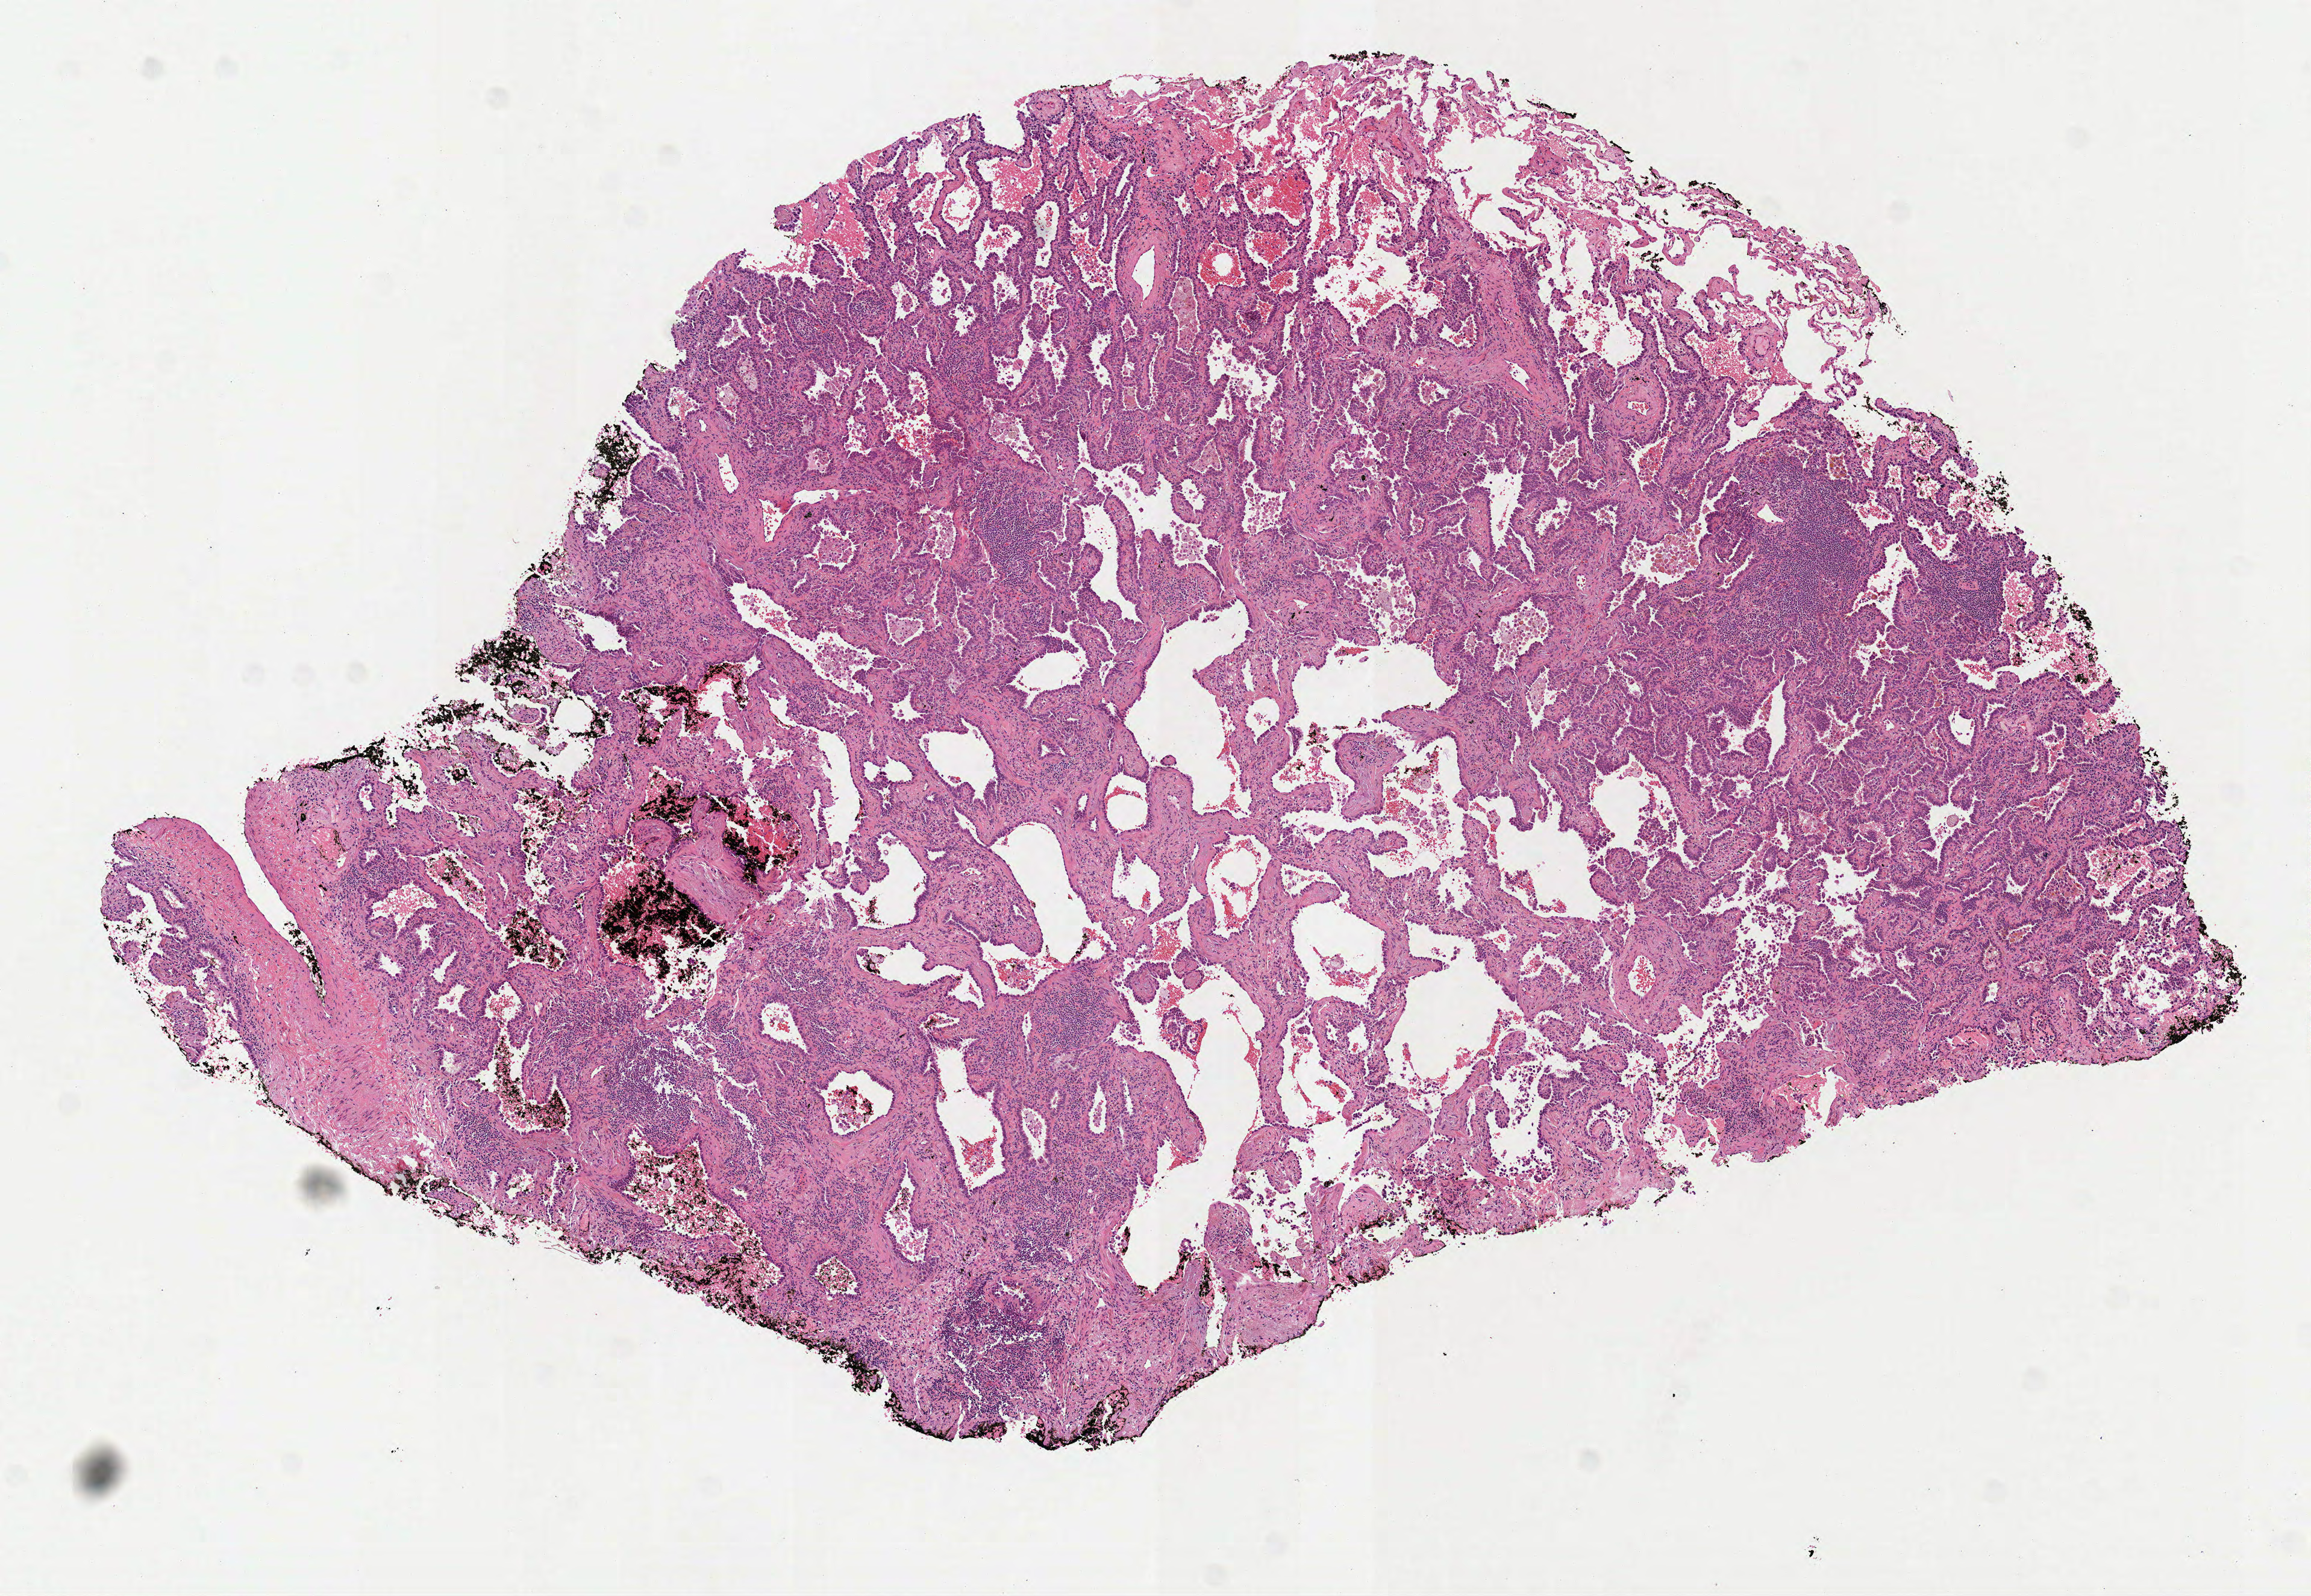
Digitized H&E-stained tissue section (whole slide) — shown as a low-resolution overview of the whole scanned area (about 7.7 x 5.3 mm); formalin-fixed paraffin-embedded (FFPE) diagnostic section; primary tumour sample from the lung. Patient: female, age at initial diagnosis 60 years.
- laterality: right
- AJCC pathologic stage: IA (7th edition)
- diagnosis: Adenocarcinoma, NOS (upper lobe, lung)
- TNM: T1a N0 MX